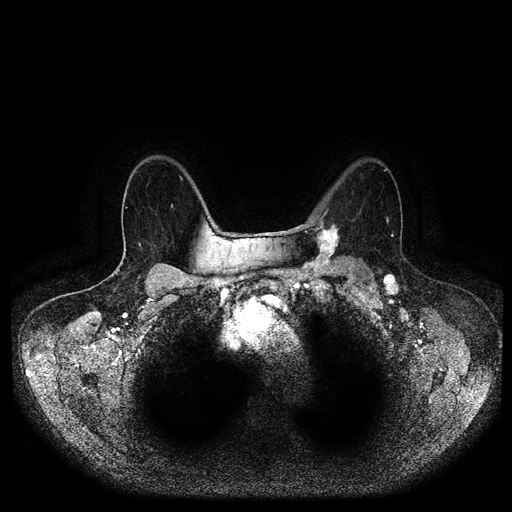
Breast MRI (dynamic contrast-enhanced, multi-phase), one axial slice; position 67 of 116 along the scan axis; dynamic contrast-enhanced series, time point 2 of 5 at this slice position (early post-contrast); 1.5 T; TE 2.6 ms, TR 5.2 ms; 512 × 512 image matrix, field of view 380 × 380 mm. Female patient, age 69 years.
Structures marked on this image (semi-automatic segmentation, software-assisted and operator-edited):
- breast lesion (labelled 'tumour' in the annotation; benign lesions carry a separate 'benign' label): box from (x=300, y=221) to (x=344, y=274) px